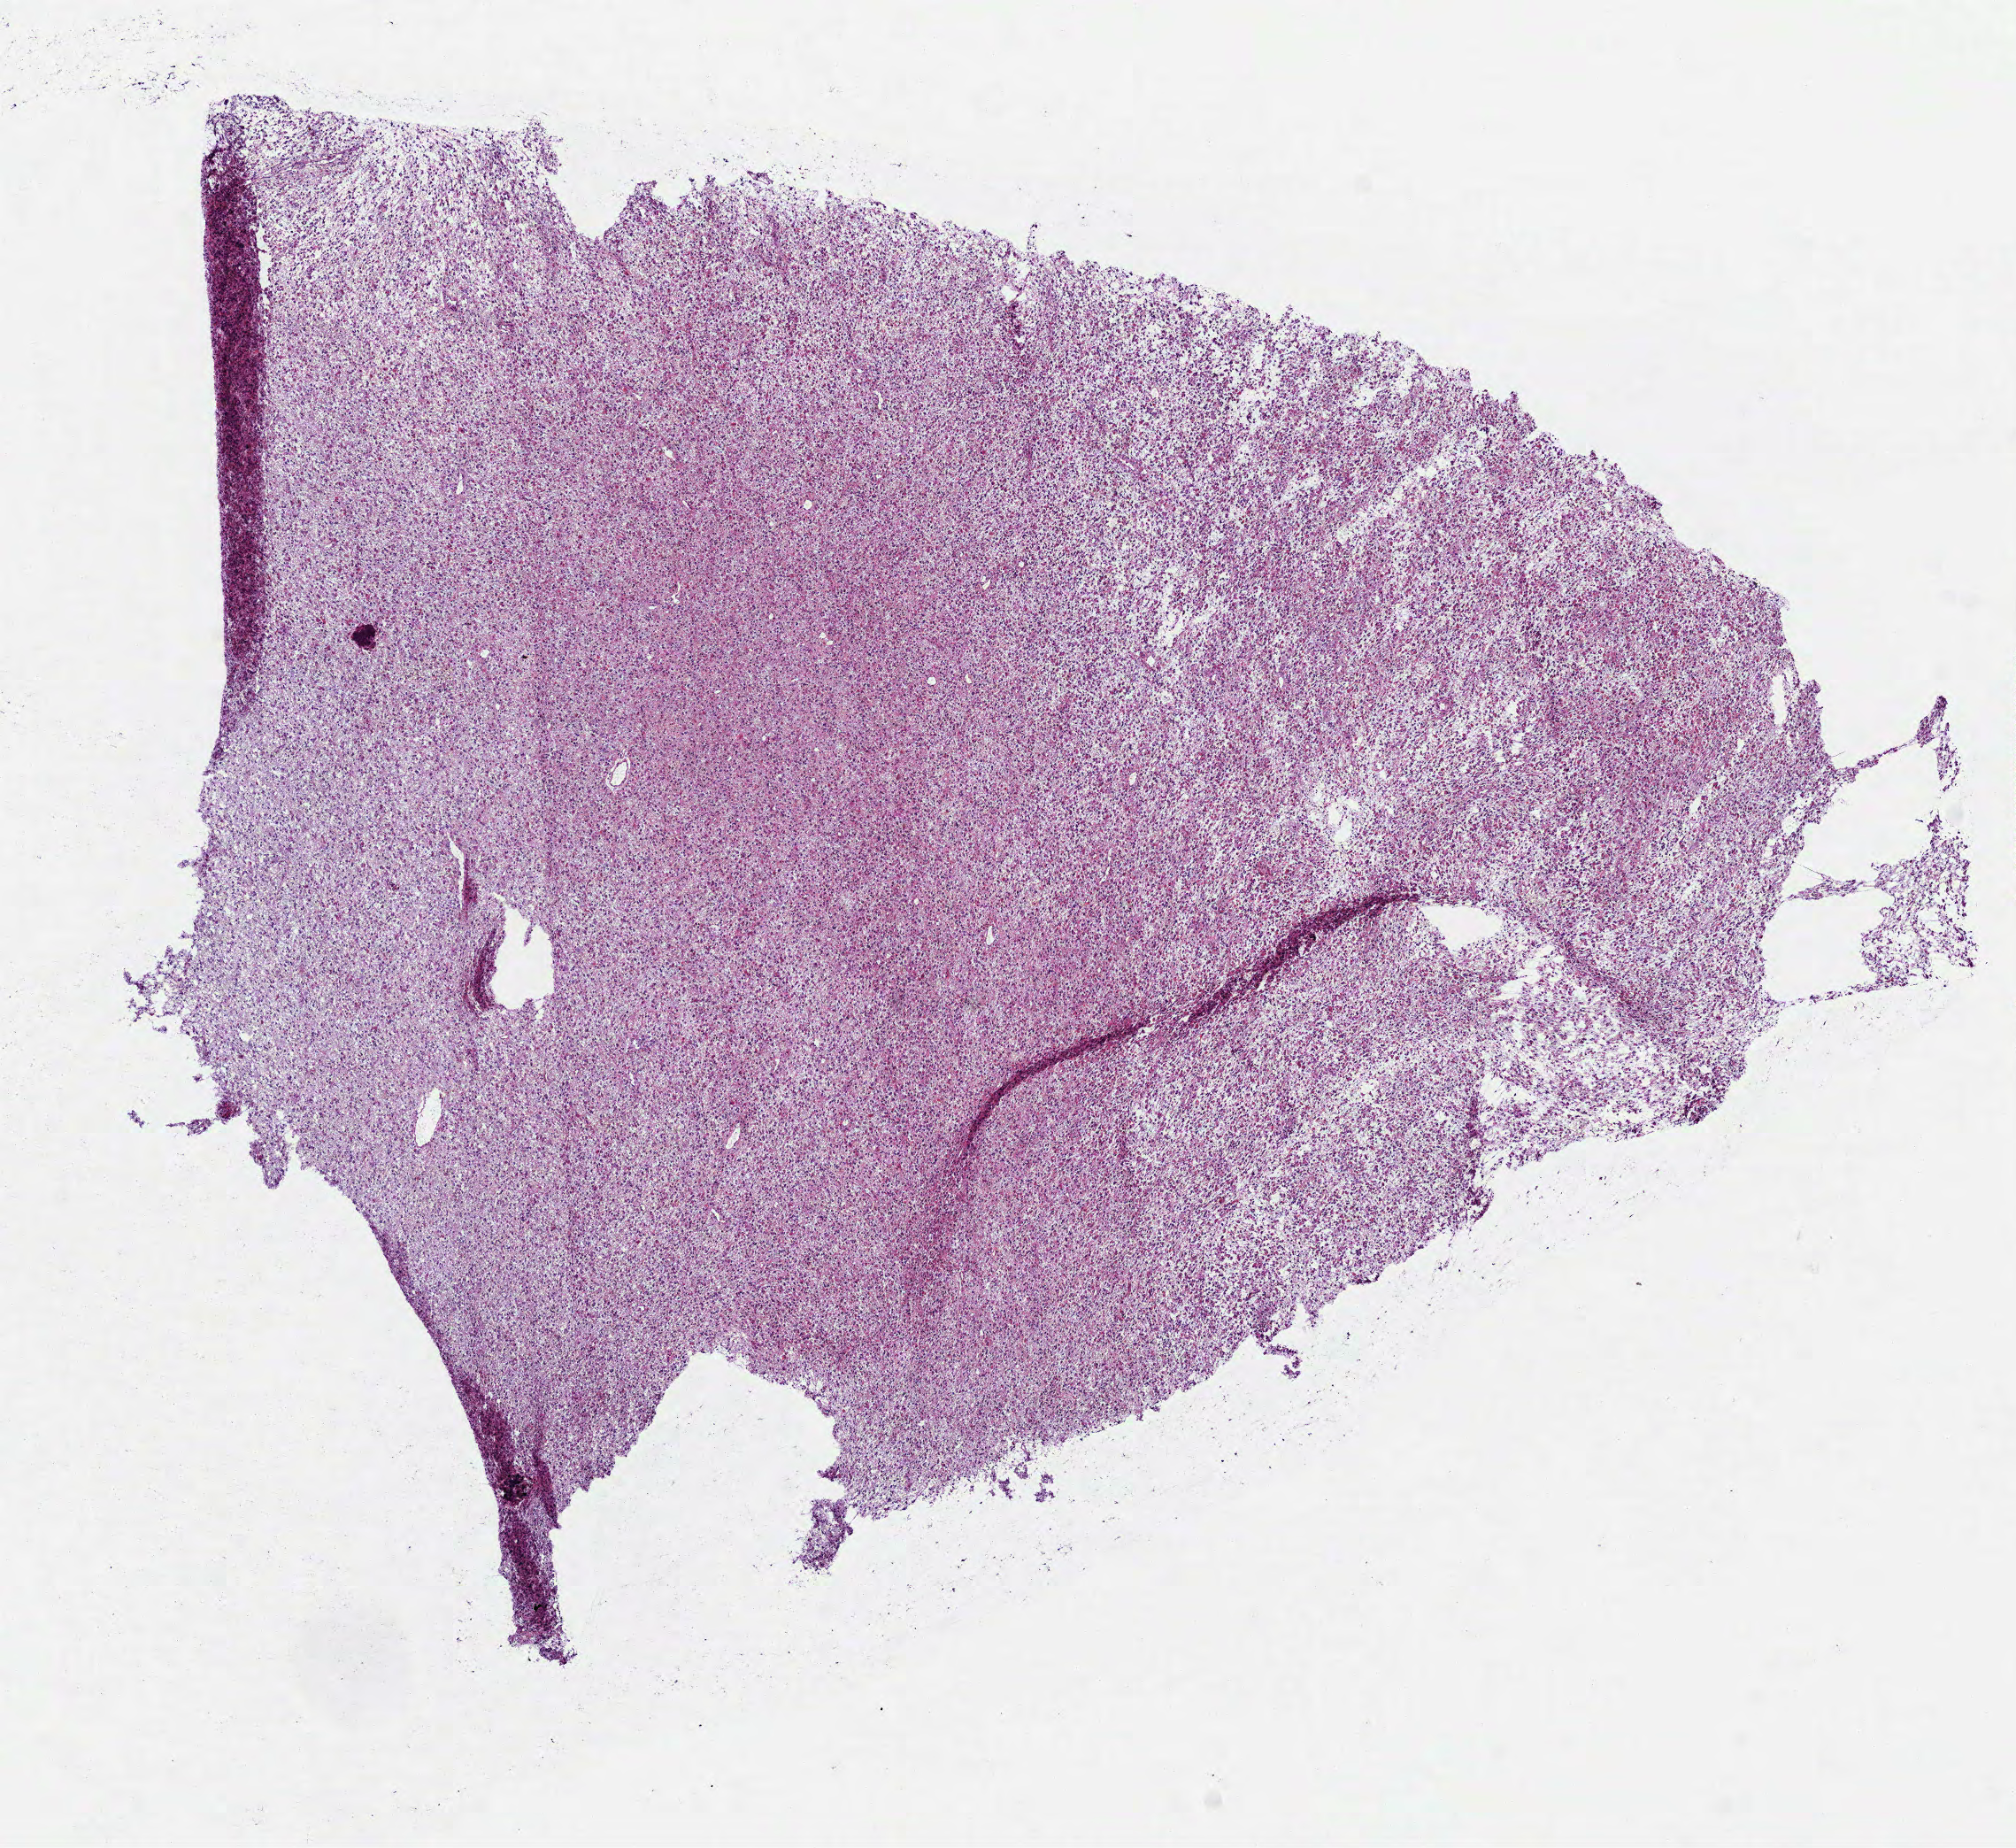
Hematoxylin and eosin (H&E) stained whole-slide image, shown as a low-resolution overview of the whole scanned area (about 9.2 x 8.4 mm, acquisition: 40x scan); frozen section from the top of the tissue portion; sample: primary tumour, brain. Patient: male, age at initial diagnosis 25 years. Histologic grade: G3 (poorly differentiated). Pathologist review of this section (percent, as recorded): tumour cells 100%, tumour nuclei 80%, normal cells 0%, stromal cells 0%, necrosis 0%.
Pathologic diagnosis: Mixed glioma (cerebrum).